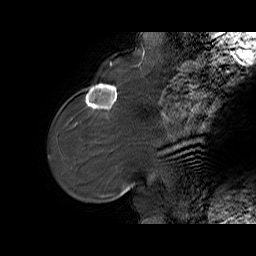
Breast MRI (dynamic contrast-enhanced), one sagittal slice; position 17 of 65 along the scan axis; dynamic contrast-enhanced series, time point 2 of 6 at this slice position (early post-contrast); 1.5 T; TE 5.7 ms, TR 32.9 ms; 4 mm slice thickness; 256 × 256 image matrix, field of view 230 × 230 mm. Female patient. Case-level facts recorded for this patient, not image findings: setting: breast cancer imaged before/during neoadjuvant chemotherapy; receptor status: HER2-positive.
Annotated regions visible in this slice (semi-automatically segmented with operator editing):
- analysis volume of interest (the breast-tissue region the enhancement analysis was run in; not a lesion): bounding box [x1, y1, x2, y2] px = [76, 77, 125, 128]
- tumour enhancement mask (voxels above the 100 % enhancement threshold inside the analysis volume of interest): [85, 83, 117, 109]